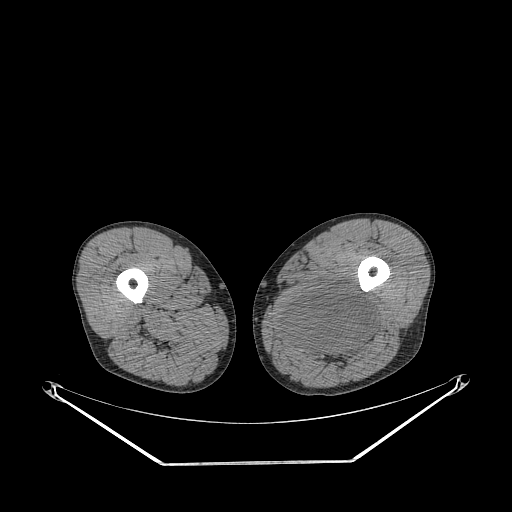
CT of an extremity soft-tissue mass (from a PET/CT study), one axial slice; slice 245 of 267 in the series (ordered by position); reconstruction kernel STANDARD; soft-tissue window (W 400 / L 40 HU); 512 × 512 image matrix, field of view 500 × 500 mm. Male patient. Case-level facts recorded for this patient, not image findings: histological type: undifferentiated pleomorphic liposarcoma; grade: high; site of the primary tumour: left thigh.
Outlined on this slice (expert contour drawn on MRI and transferred to this co-registered scan by the dataset authors):
- gross tumour volume including surrounding oedema: bounding box [x1, y1, x2, y2] px = [276, 286, 375, 362]
- gross tumour volume (mass): [285, 286, 375, 352]